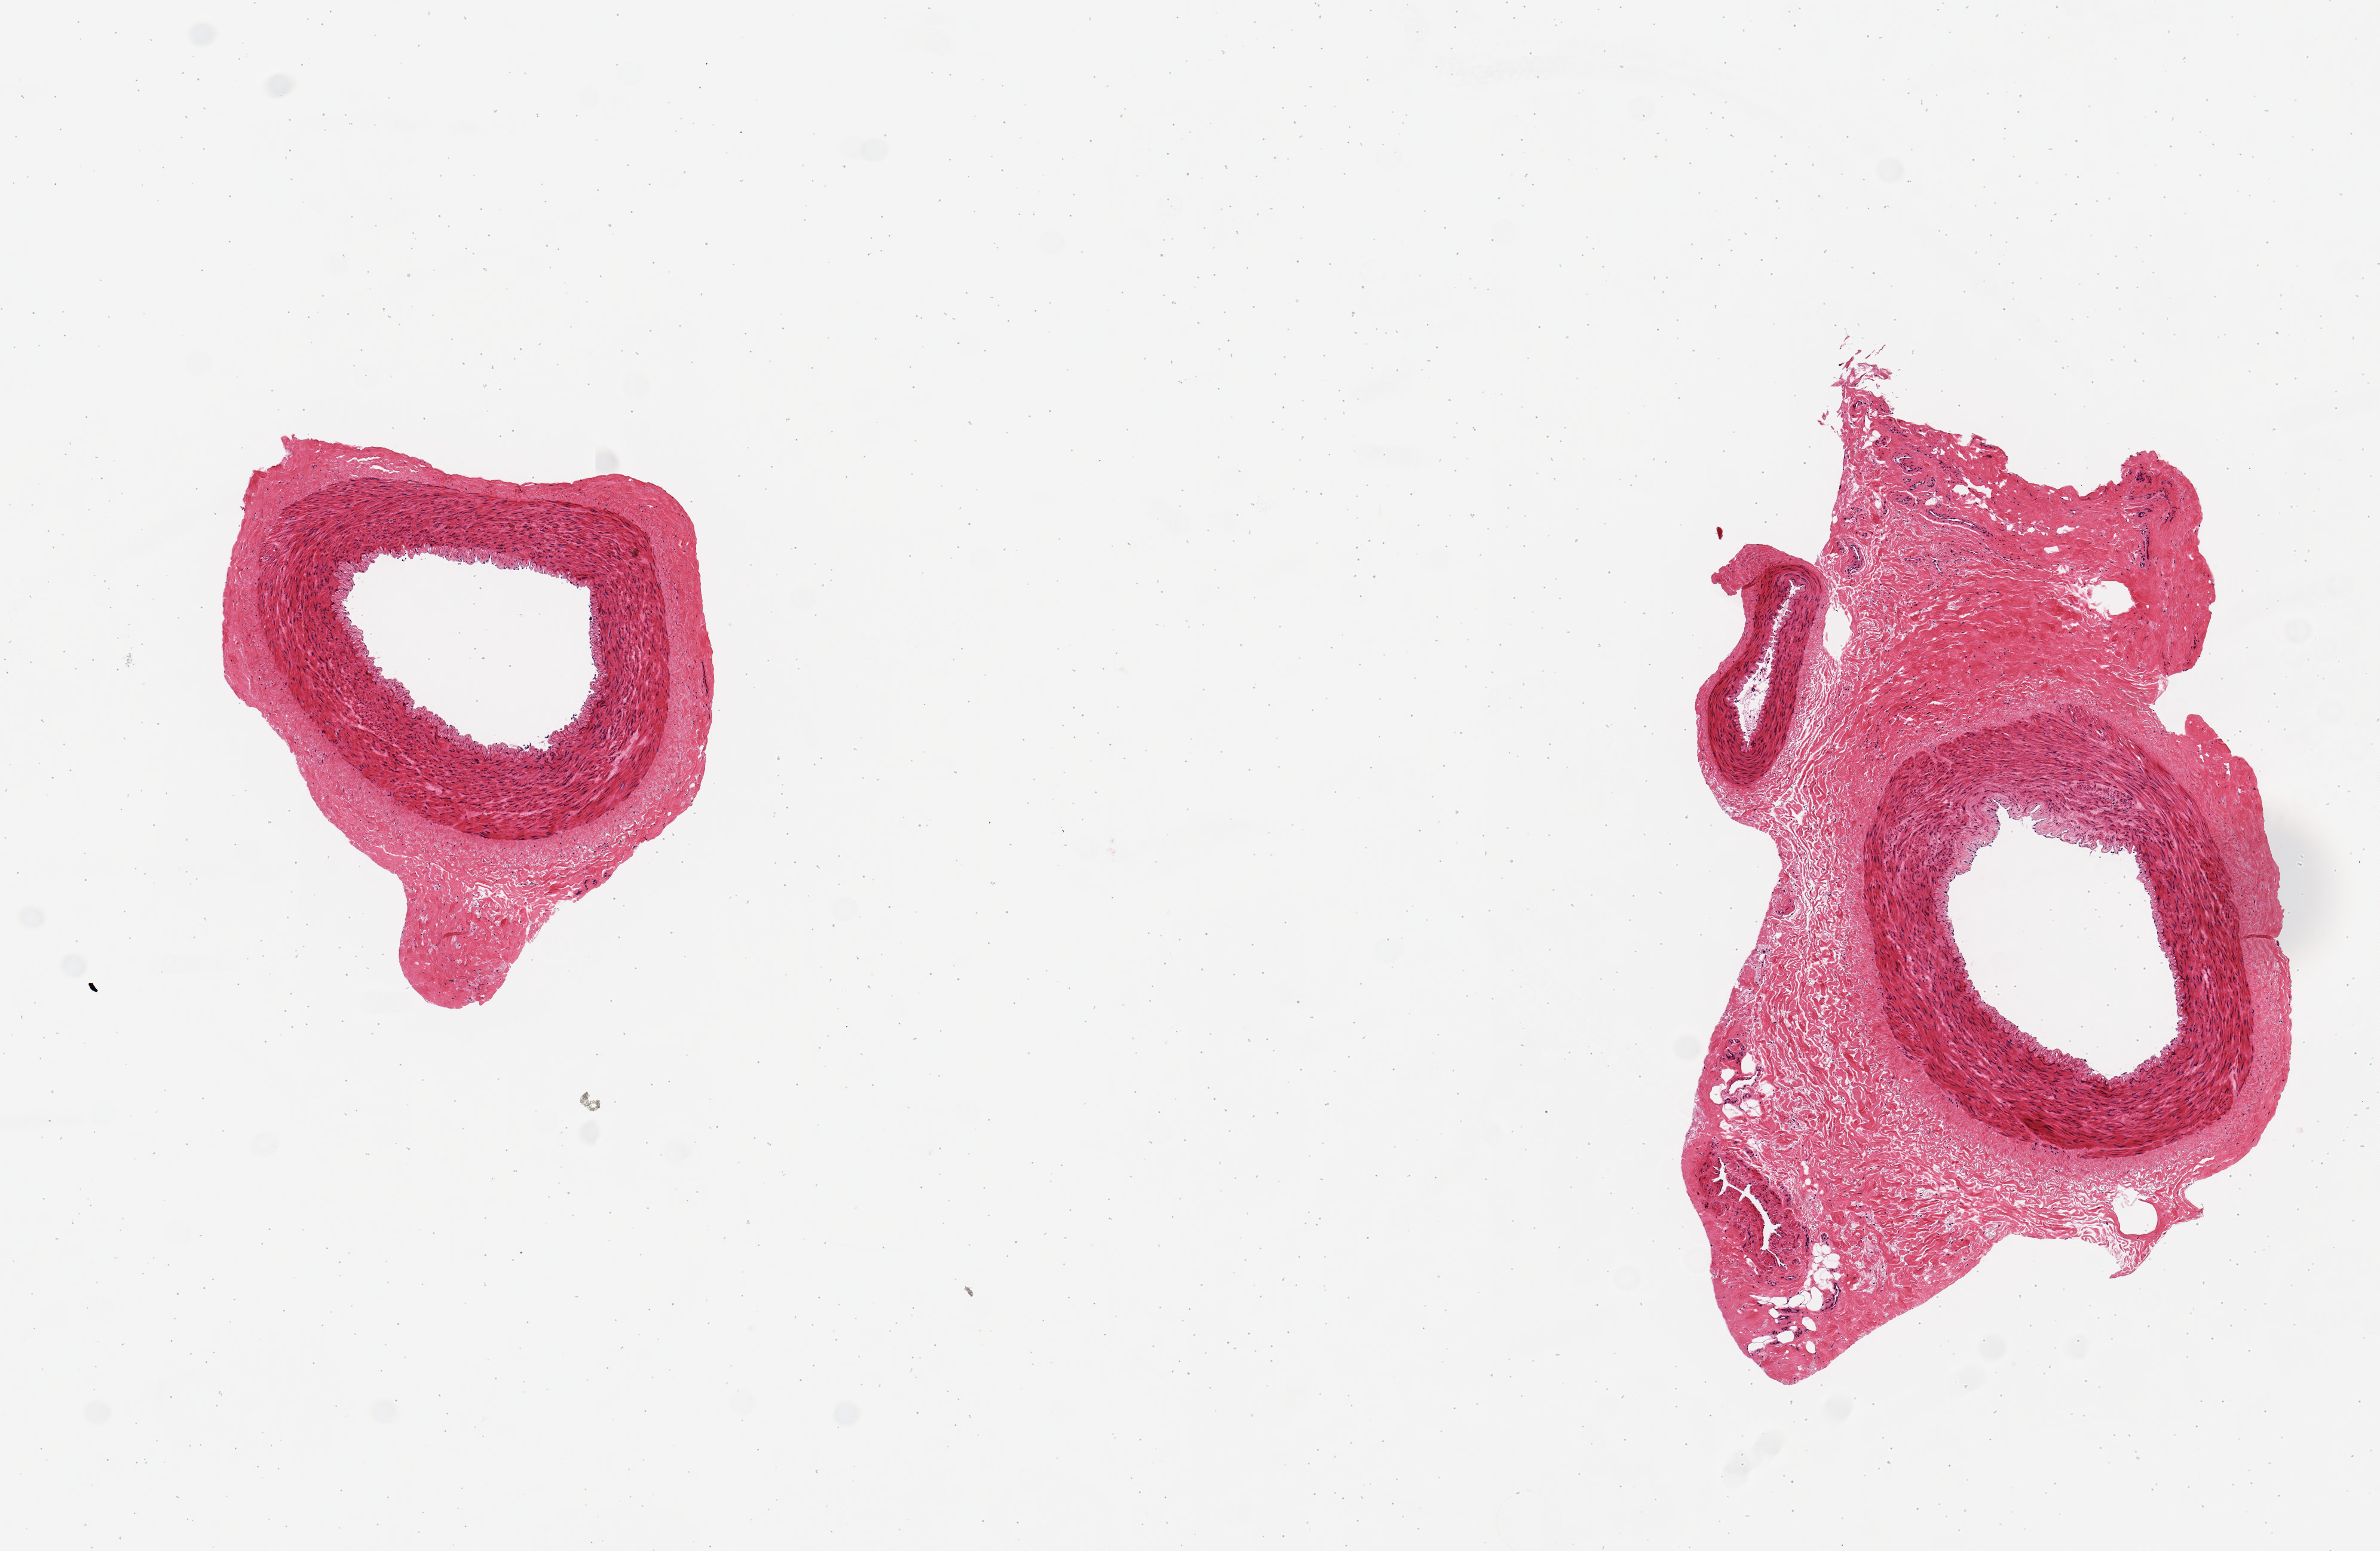
Whole-slide image, hematoxylin and eosin (H&E) stain, a low-resolution overview of the entire scanned area, about 7.9 x 5.1 mm, PAXgene-fixed, paraffin-embedded tissue, target tissue: tibial artery, tissue donor sample.
Pathologist's review note for this sample: 2 pieces: 3x2 & 1.8x1.7 mm; larger contains 2 normal arteries, 1 small vein & 40% surrounding fibrous stroma; Smaller artery has 20% stroma.